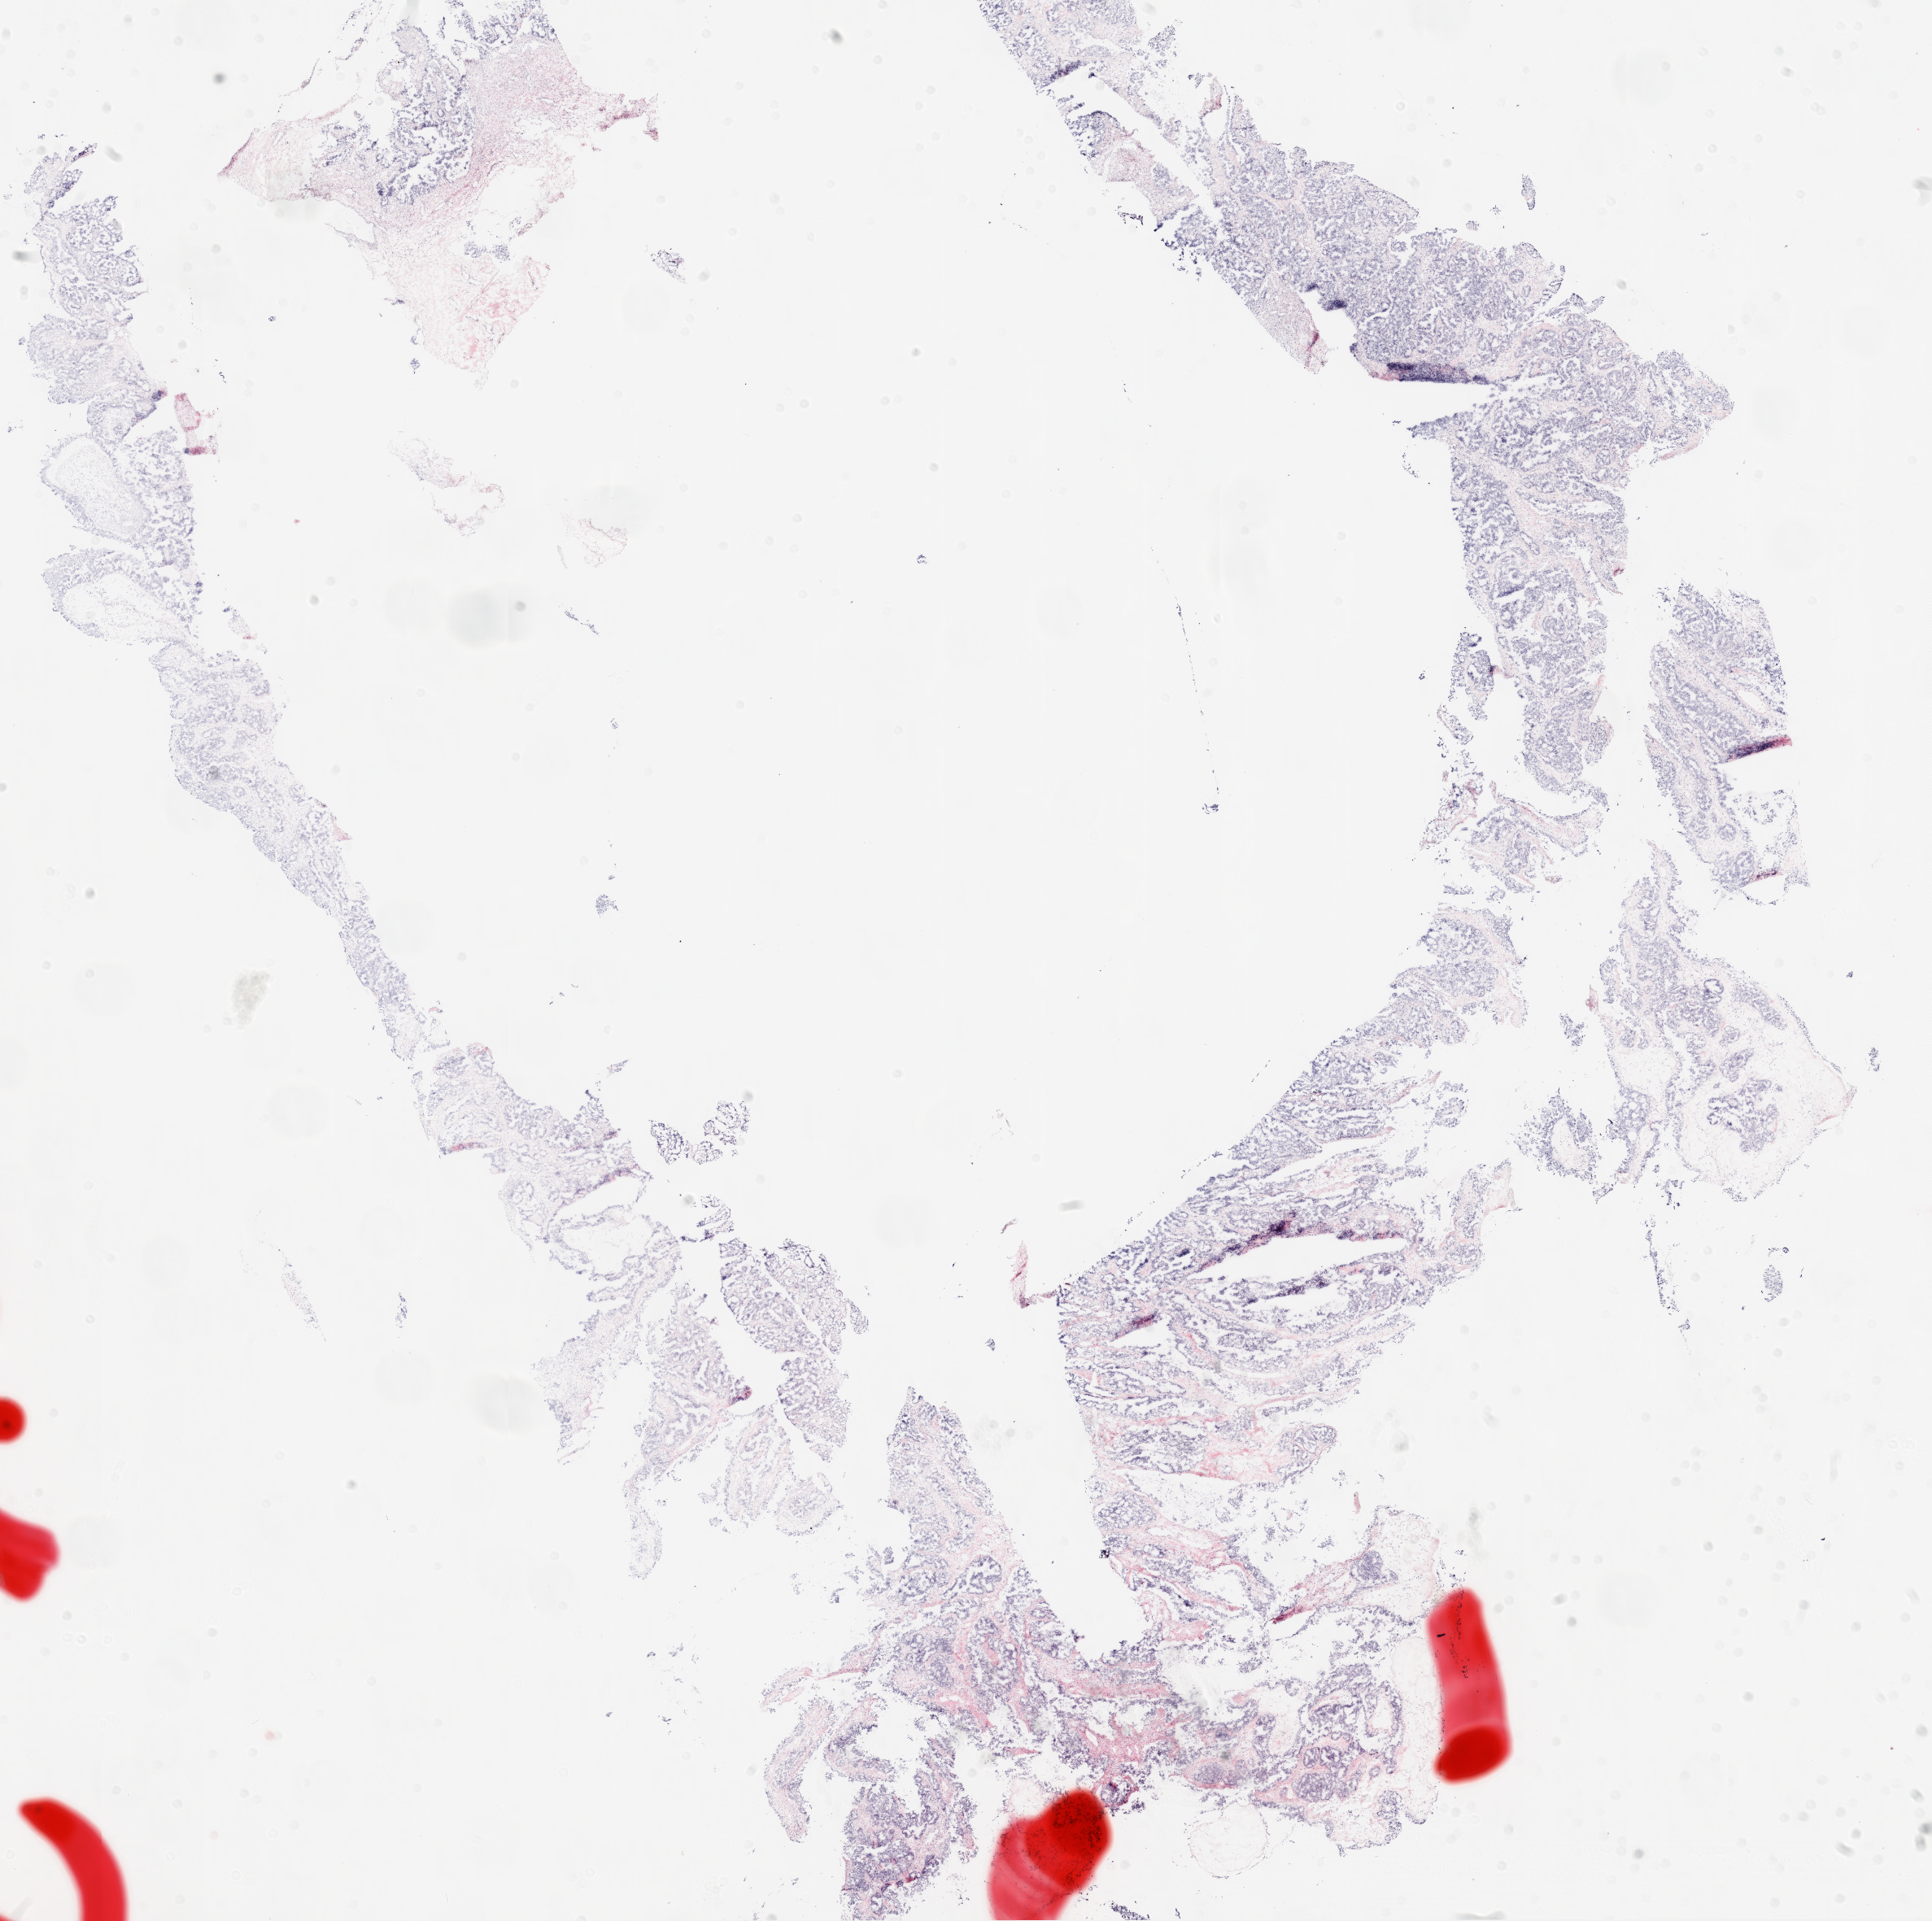
Whole-slide histology image, H&E-stained, low-resolution overview of the scanned area, about 19.1 x 19.0 mm (from a 20x scan); frozen section from the top of the tissue portion; primary tumour sample from the ovary. Female patient; age at initial diagnosis 69 years. Histologic grade: G3 (poorly differentiated). Composition of this section per pathologist review: tumour cells 90%, tumour nuclei 90%, normal cells 0%, stromal cells 10%, necrosis 0%.
FIGO stage: IC. Histologic diagnosis: Serous cystadenocarcinoma, NOS.